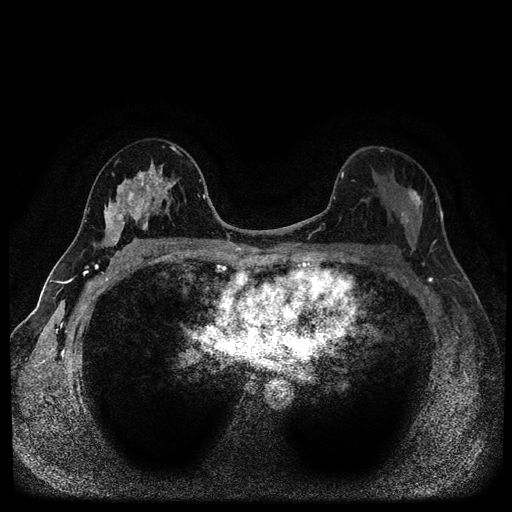
Breast MRI (dynamic contrast-enhanced, multi-phase), one axial slice. Dynamic contrast-enhanced series, time point 2 of 5 at this slice position (early post-contrast). 1.5 T. TE 2.7 ms, TR 5.4 ms. 512 × 512 image matrix, field of view 320 × 320 mm. Patient: female, 49 years.
Structures marked on this image (semi-automatic segmentation, software-assisted and operator-edited):
- breast lesion (labelled benign in the annotation): bounding box [x1, y1, x2, y2] px = [102, 159, 174, 247]